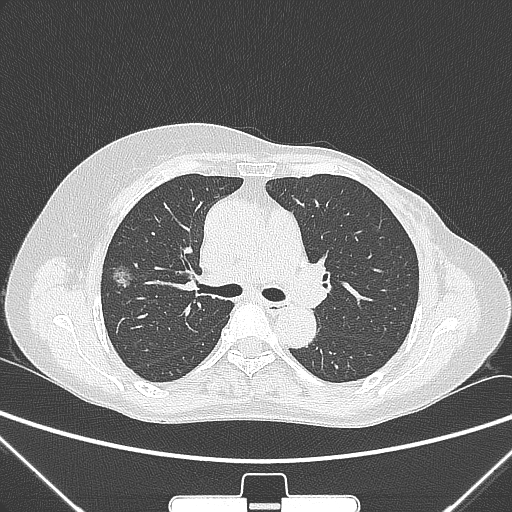
Chest CT, one axial slice; position 159 of 265 along the scan axis; lung window (W 1500 / L -600 HU); 512 × 512 image matrix, field of view 350 × 350 mm. Patient: female, 64 years. From the clinical record (not read from this slice): clinical TNM (as recorded): T1c N0 M0; histopathological grade: G1-2.
Annotated regions visible in this slice (bounding box drawn by a radiologist):
- lung tumour (recorded histology: adenocarcinoma): box from (x=108, y=259) to (x=139, y=293) px